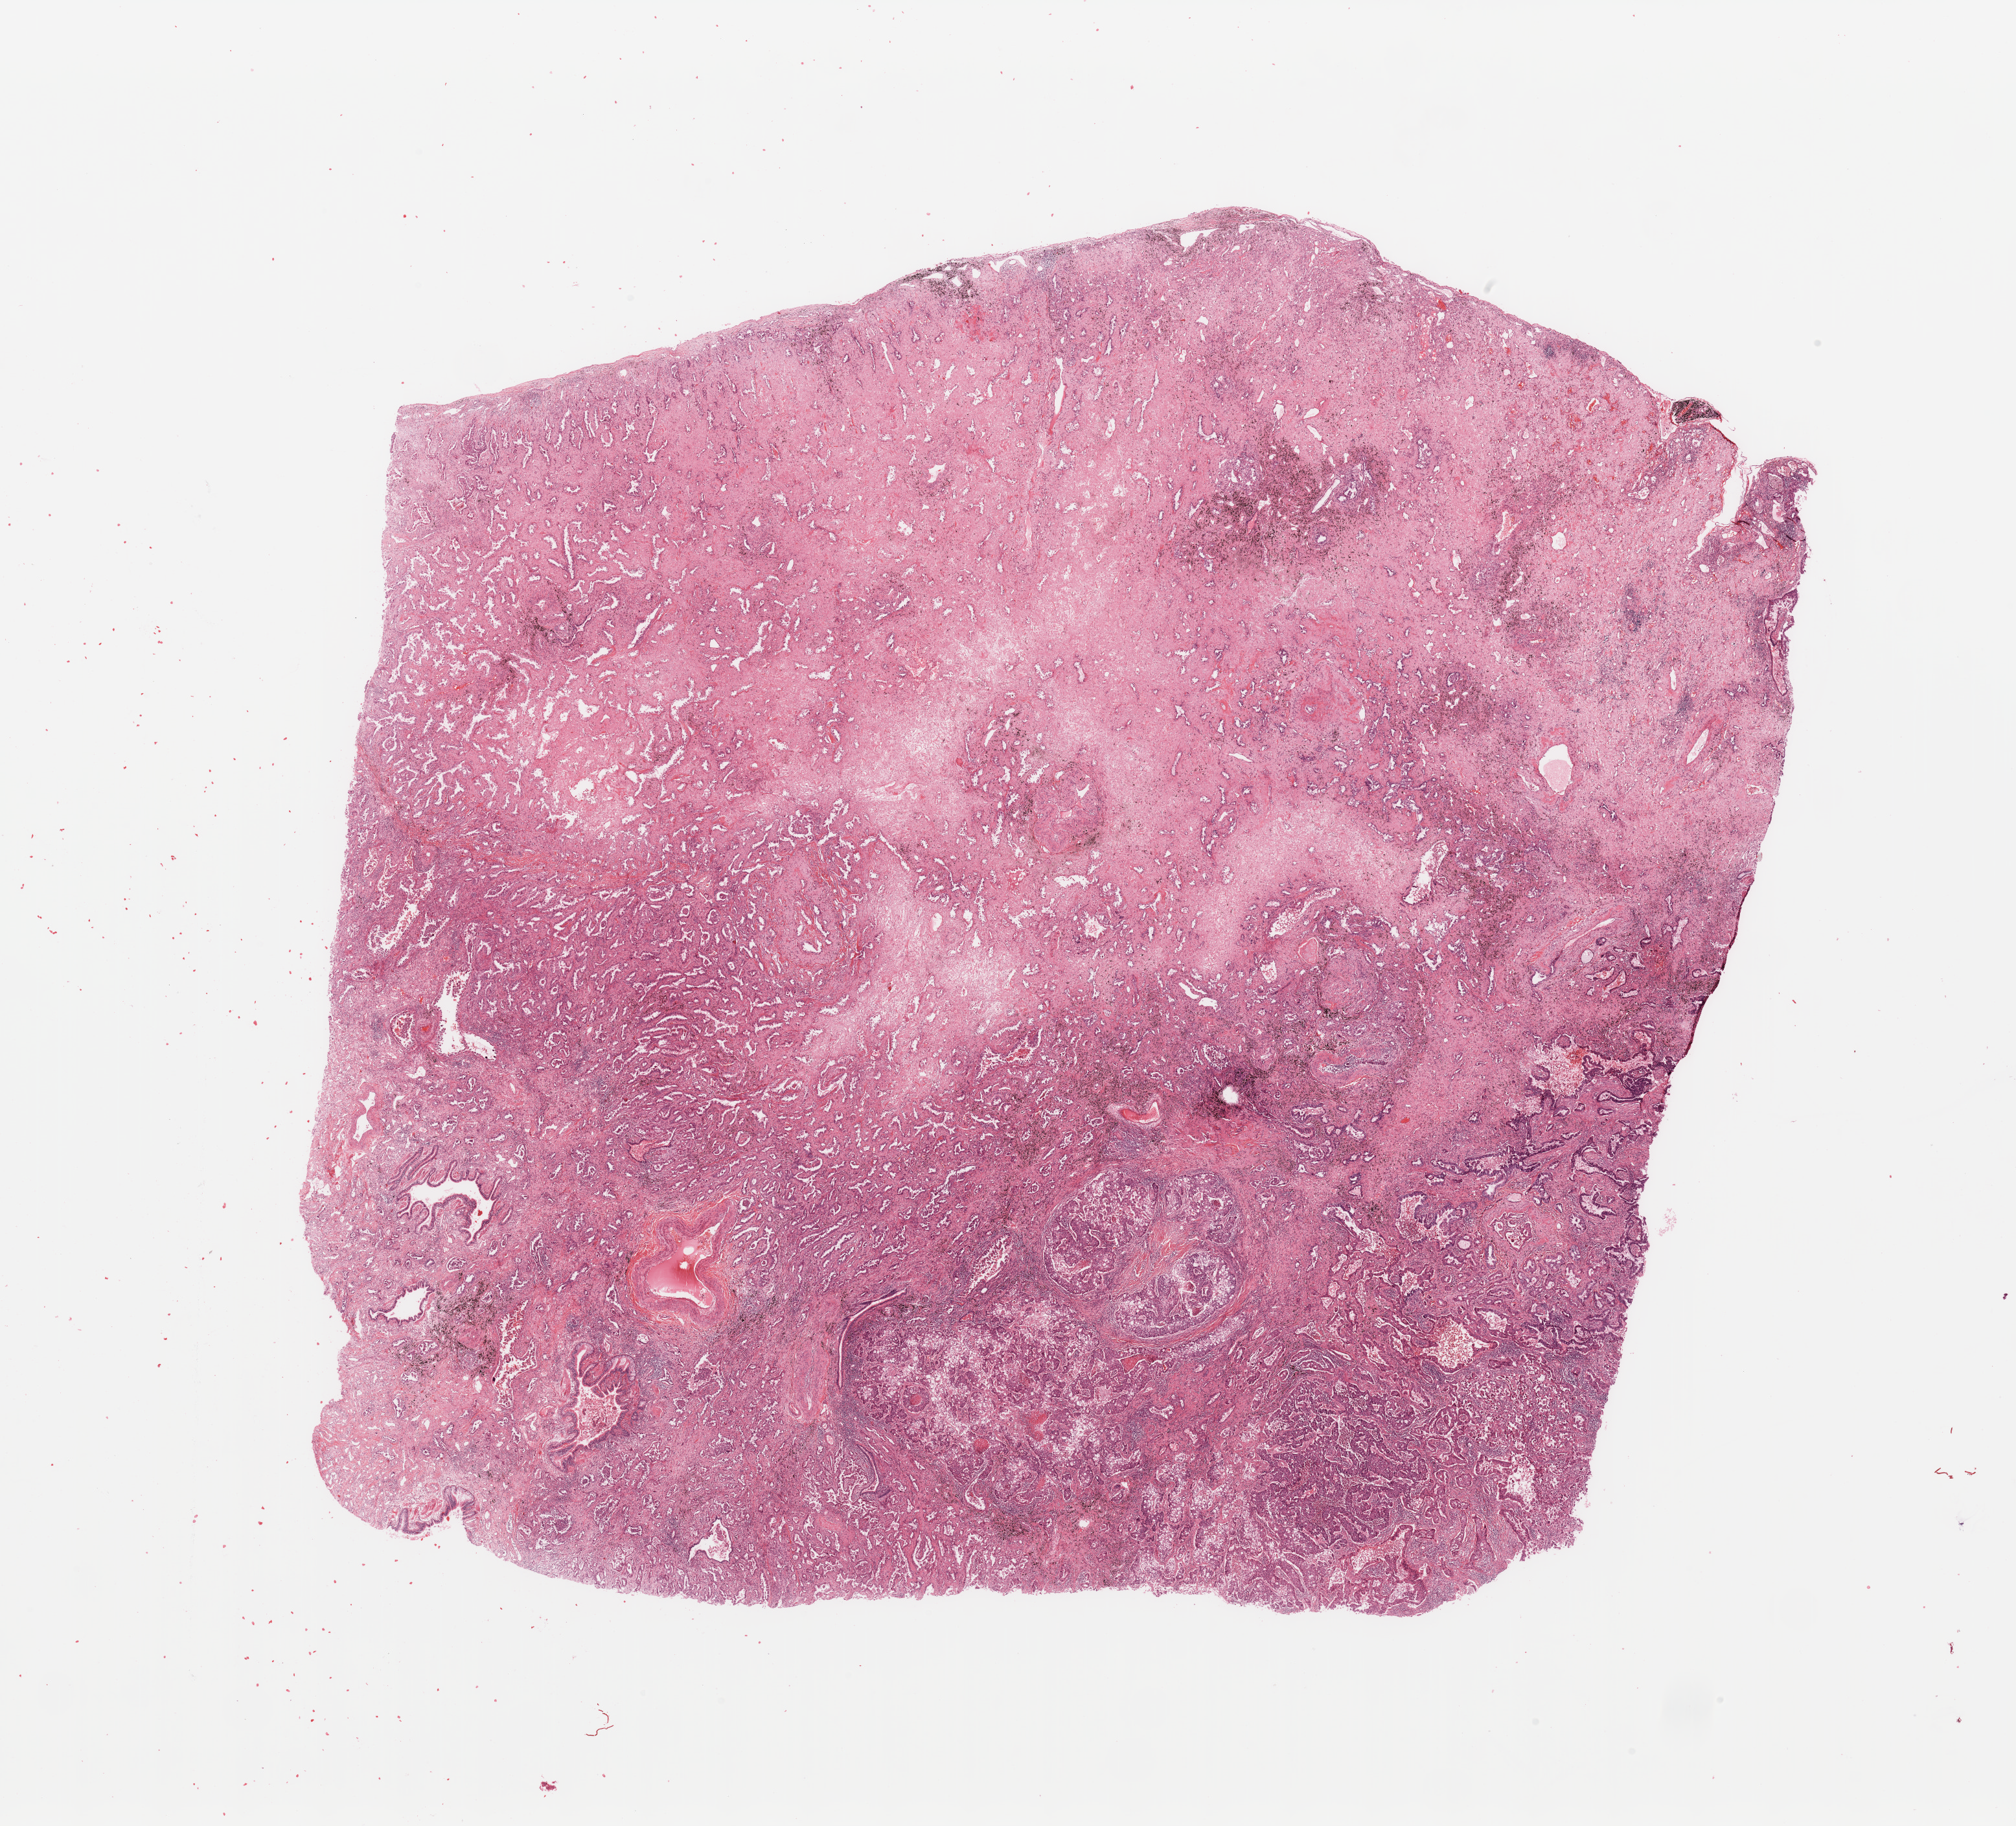
Digitized H&E tissue section (whole slide) — shown as a low-resolution overview of the whole scanned area (about 24.6 x 22.3 mm). Tumour tissue sample, sampled site: lung. Patient: female, age 72 years. Histologic grade: G2 (moderately differentiated). Pathologist review of this section (percent, as recorded): tumour nuclei 70%, necrosis 2%.
AJCC pathologic stage: IIIA. Diagnosis: Adenocarcinoma, NOS.